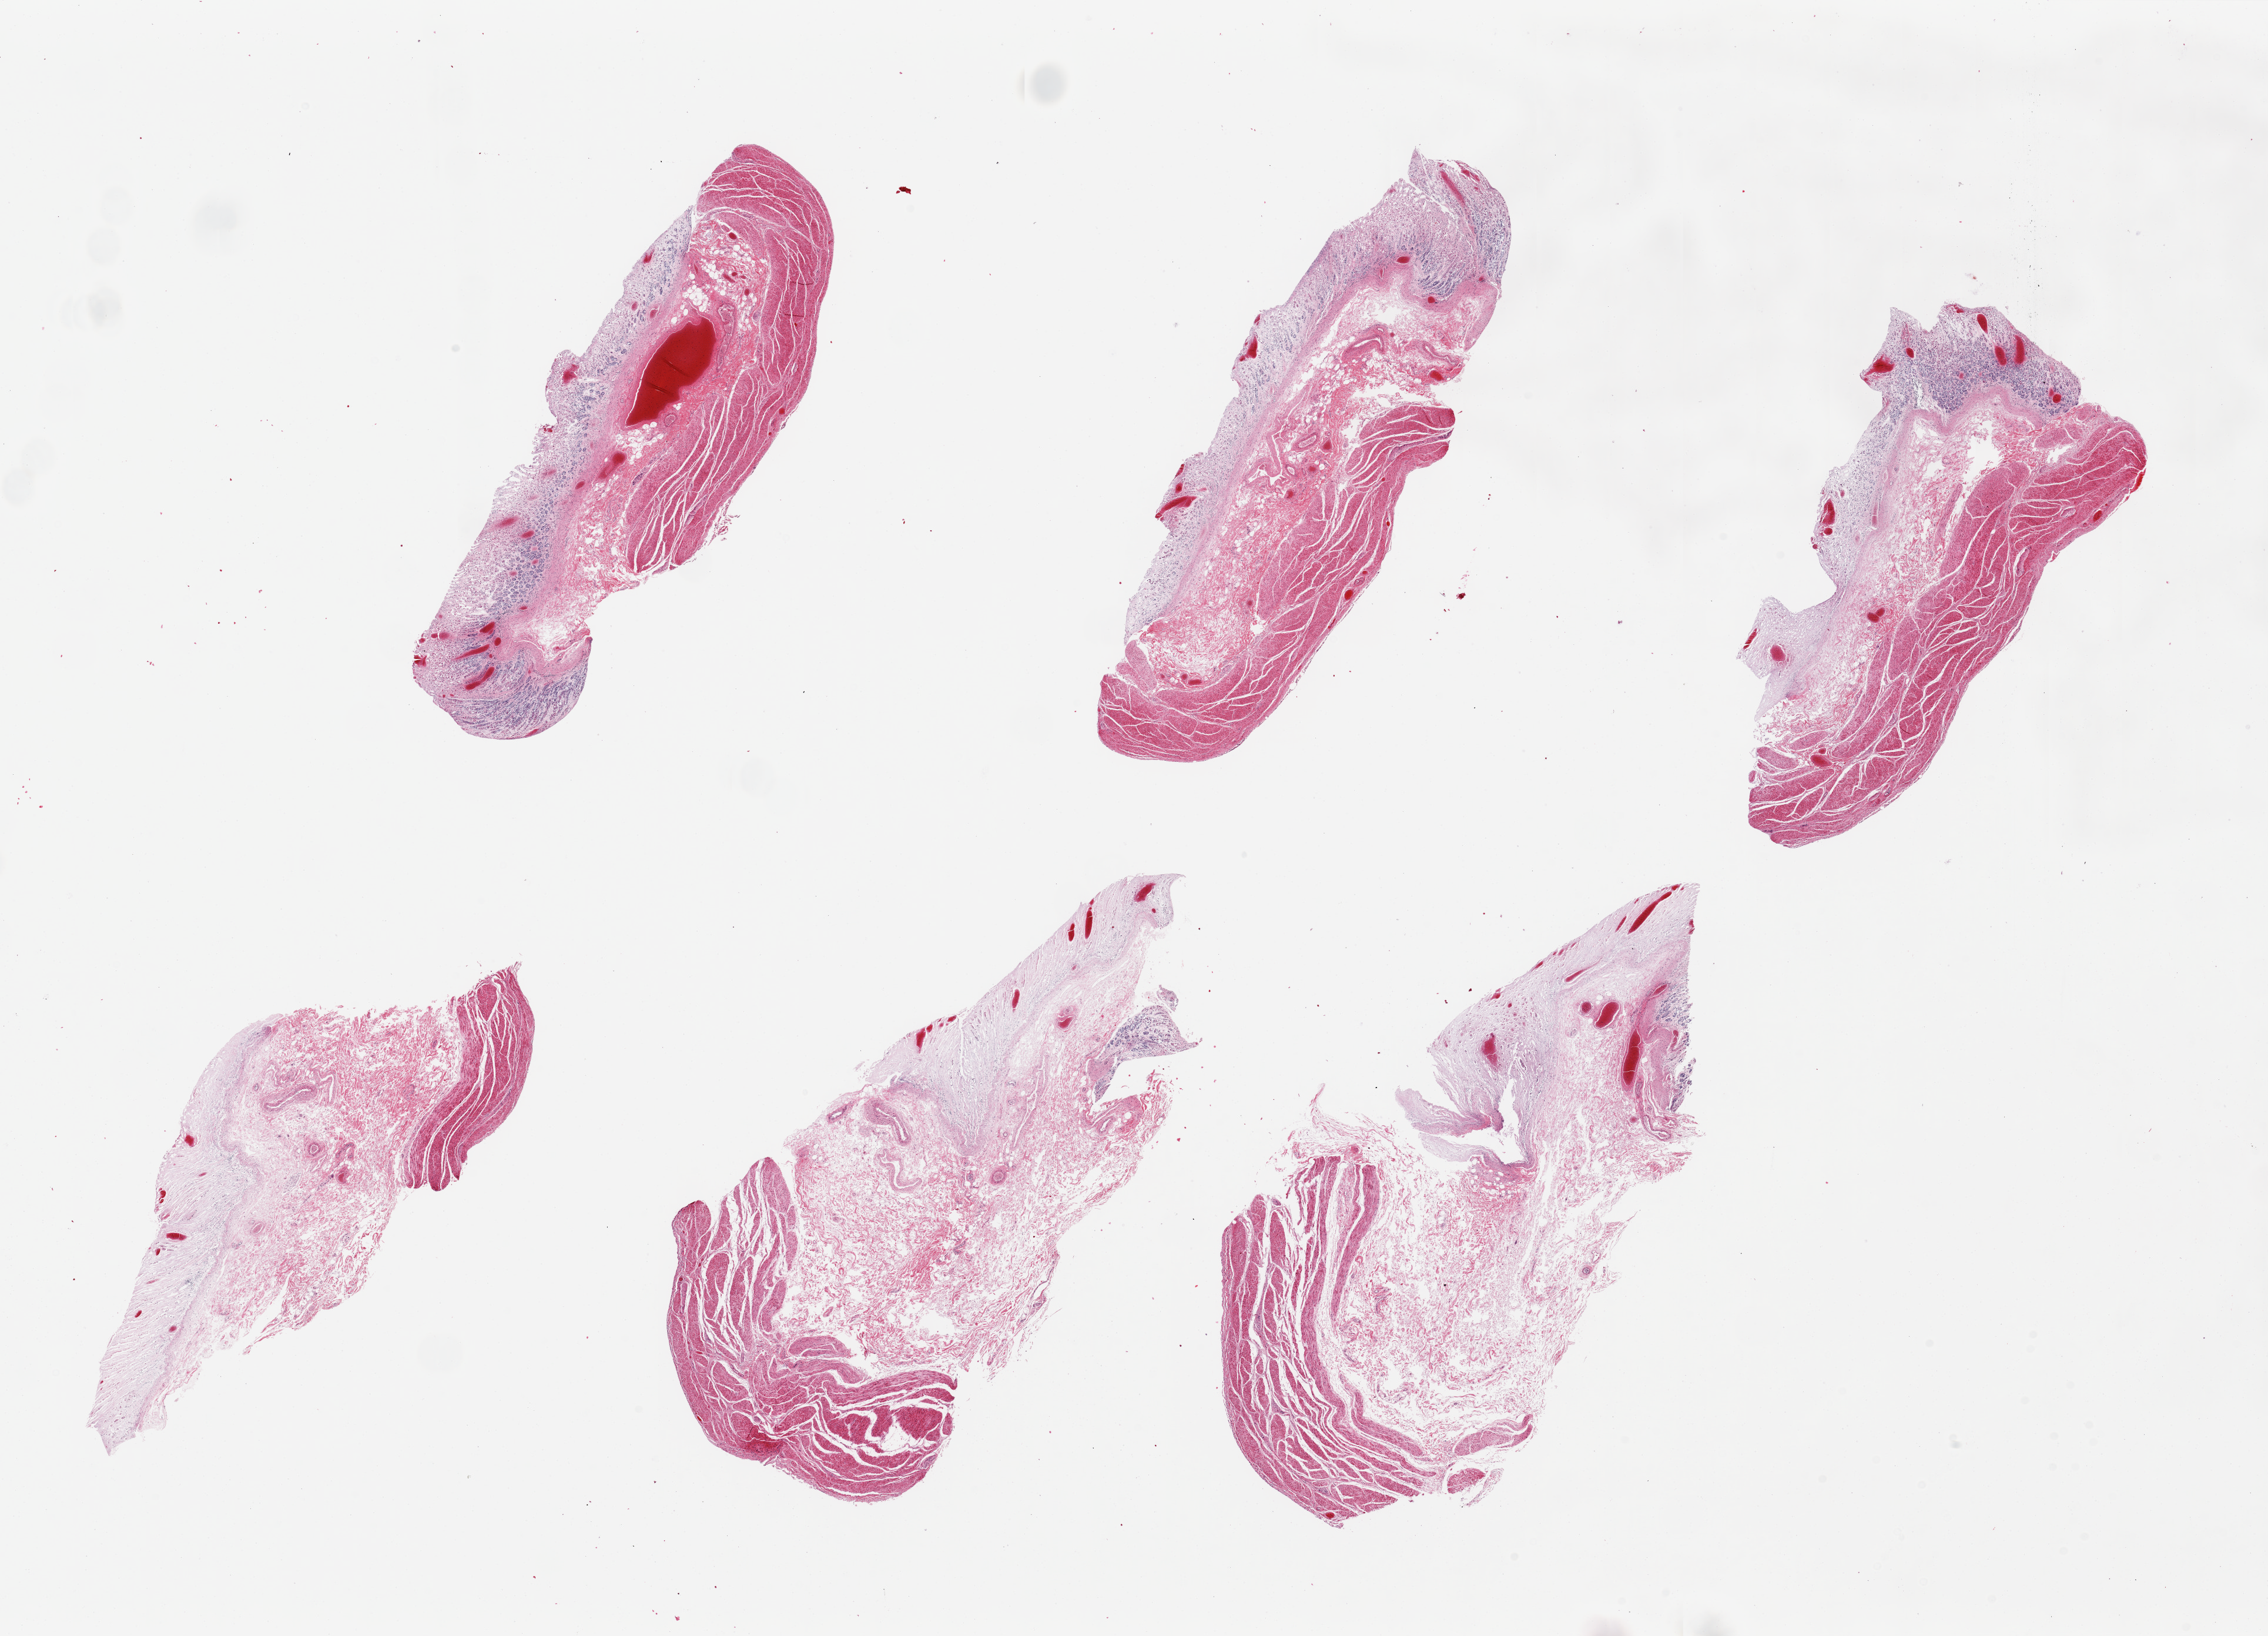
Digitized haematoxylin and eosin-stained section, brightfield — whole scanned area (about 30.5 x 22.0 mm, from a 20x scan) shown as a low-resolution overview, PAXgene-fixed paraffin-embedded (PFPE) section, sampled site (target tissue): stomach, tissue donor sample. Donor: male.
Reviewer comment on this tissue sample: 6 pieces, up to 10x5mm; mucosa completely autolyzed/sloughed.